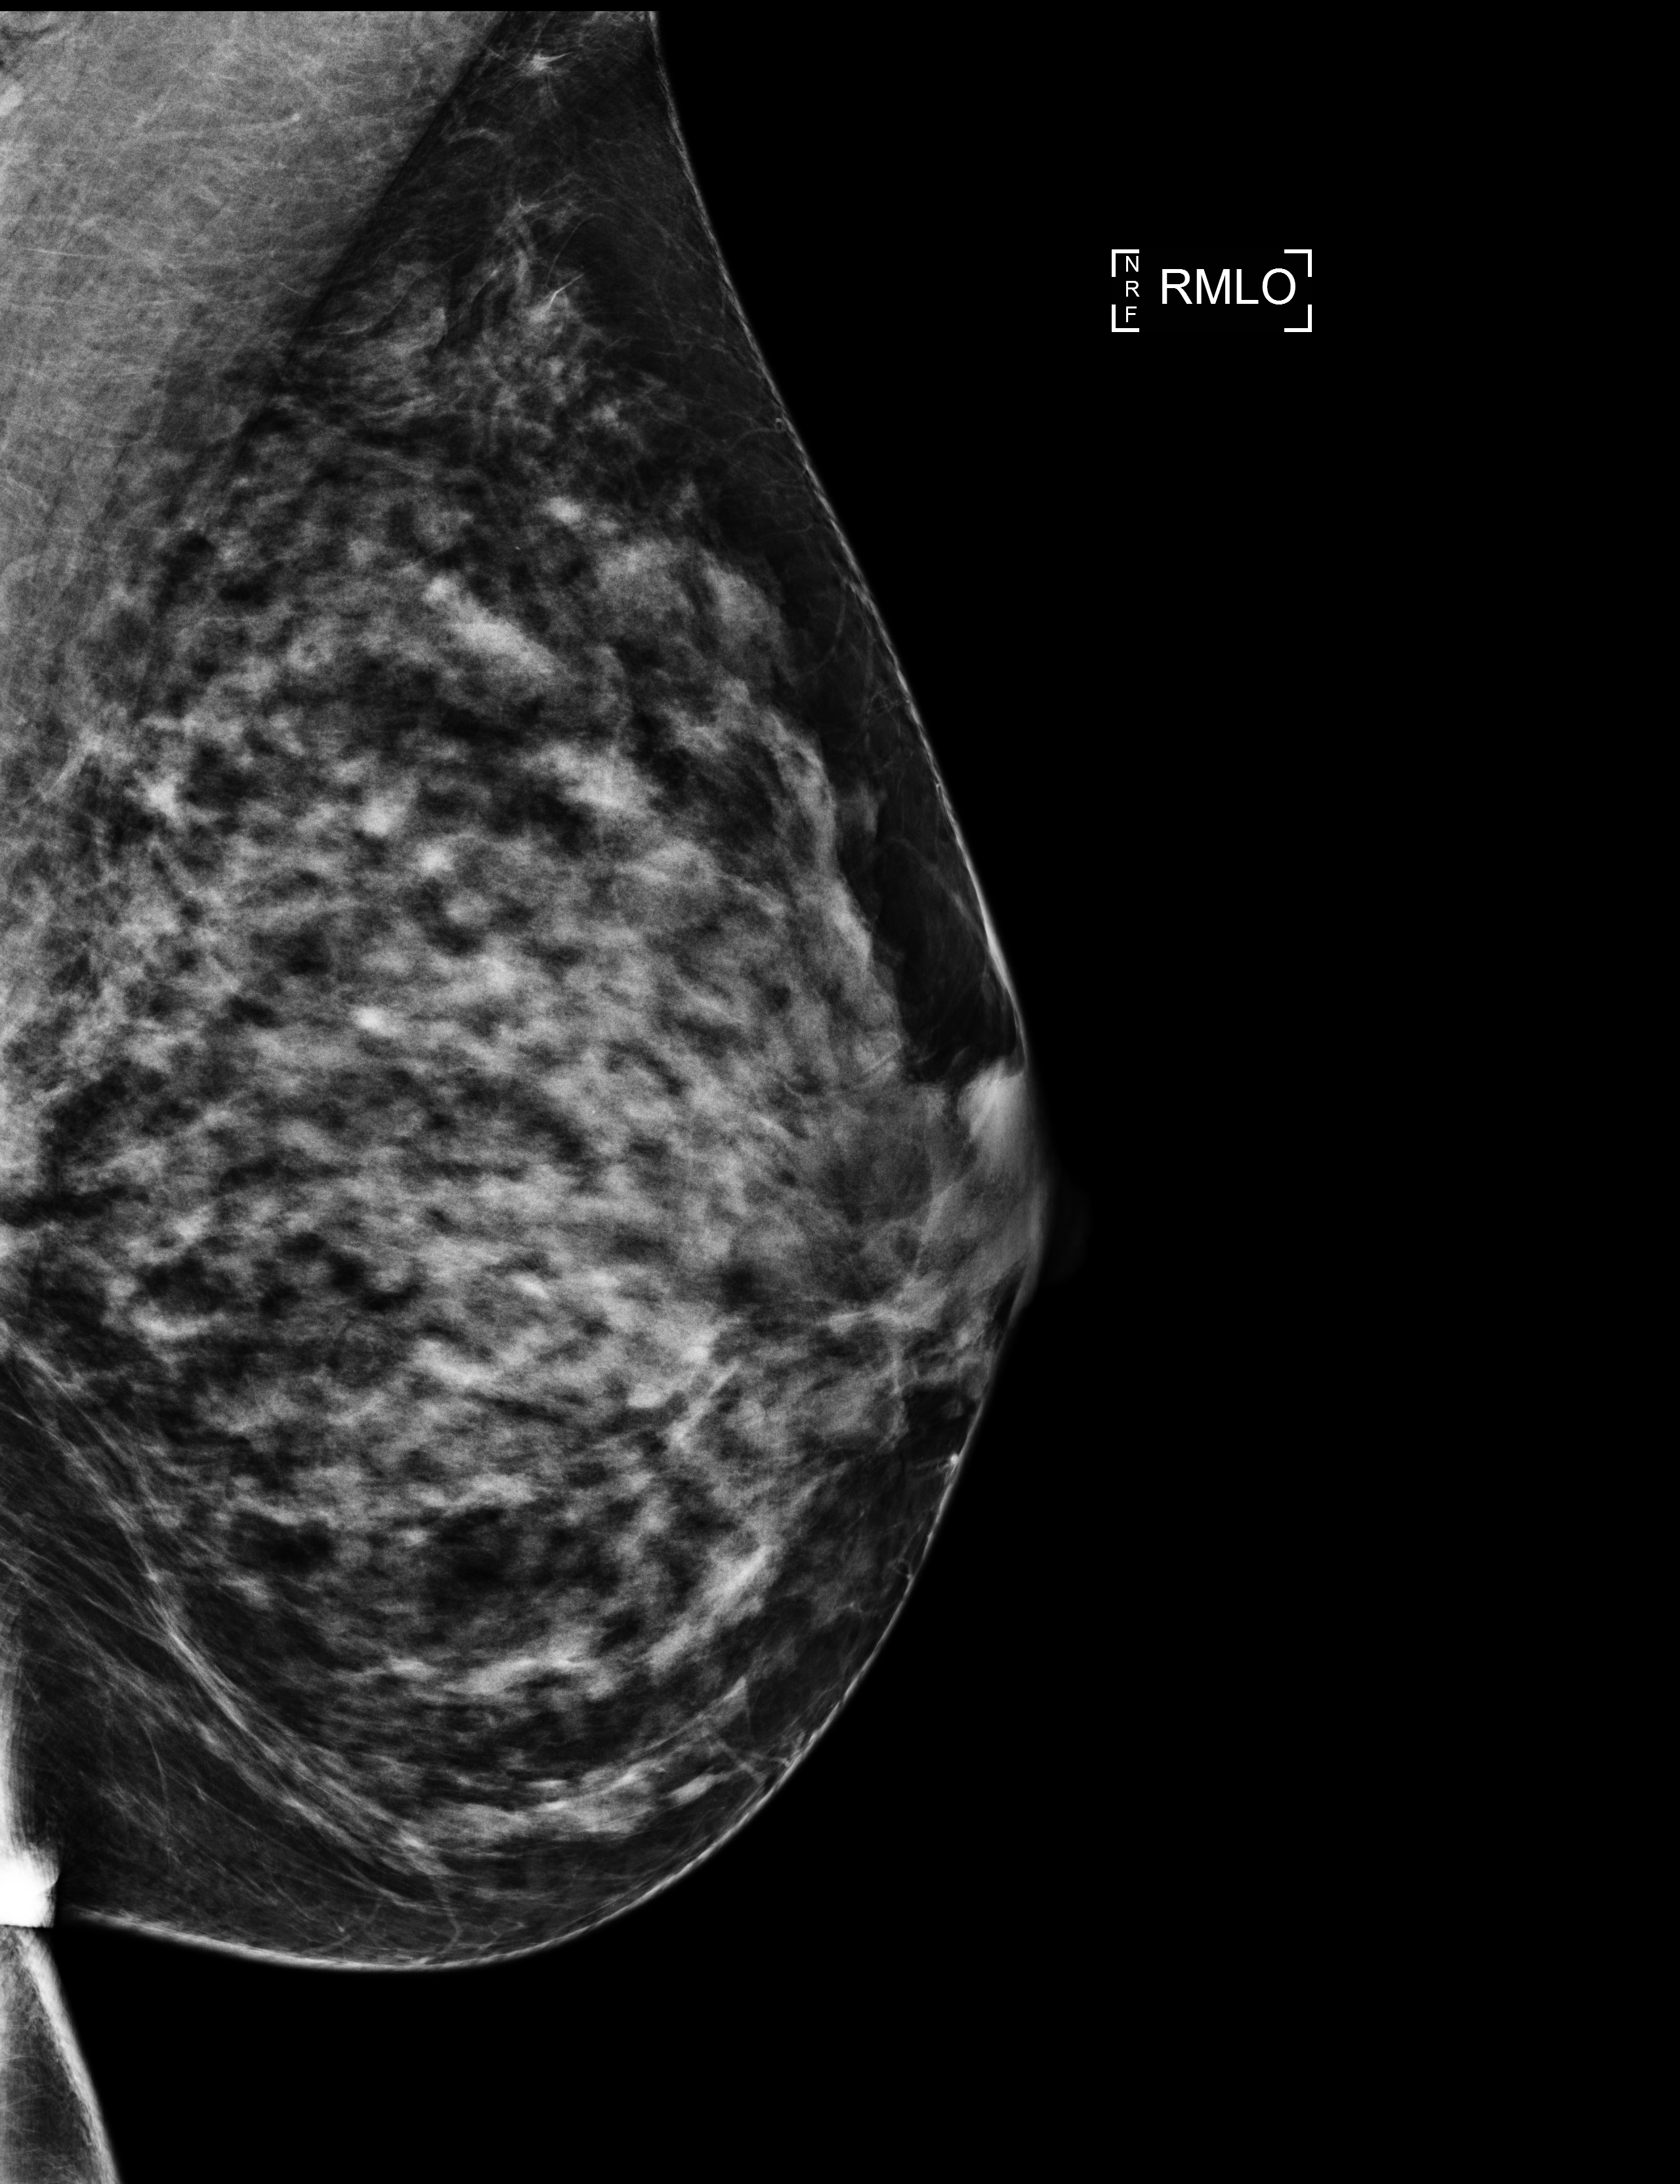
Annual screening mammography examination; system: Selenia Dimensions. Female patient, age 60 years.
Image type: full-field digital mammogram. Breast: right. Projection: medio-lateral oblique projection.